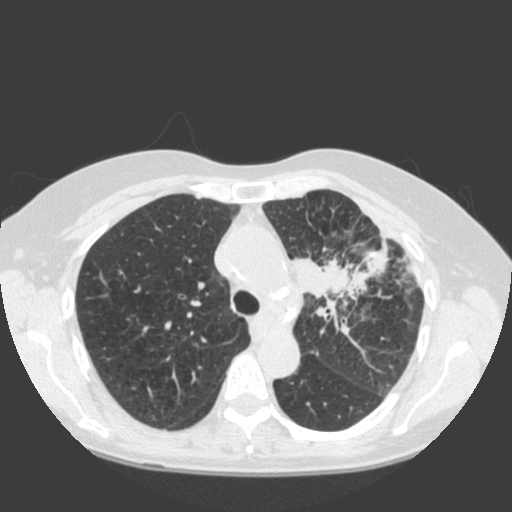
Low-dose screening chest CT, axial slice; first (baseline) screen; lung window (W 1500 / L -600 HU); 120 kVp; slice 50 of 184 in the series; 512 × 512 image matrix. Female participant, aged 66 years at enrolment. Current smoker at enrolment.
Expert reader's lesion annotation, bounding box (x1, y1, x2, y2) in pixels: (285, 237, 398, 338). Reader record for this screening exam (exam-level; its link to the box is not recorded): non-calcified nodule or mass ≥4 mm, left upper lobe, 61 × 45 mm, spiculated (stellate) margins, soft tissue attenuation. Lung cancer was diagnosed 19 days after this screen: squamous cell carcinoma, keratinizing, NOS, left upper lobe, left hilum, mediastinum, left main stem bronchus, other location, poorly differentiated (G3), stage IIIB (AJCC 6th edition), 60 mm at pathology.